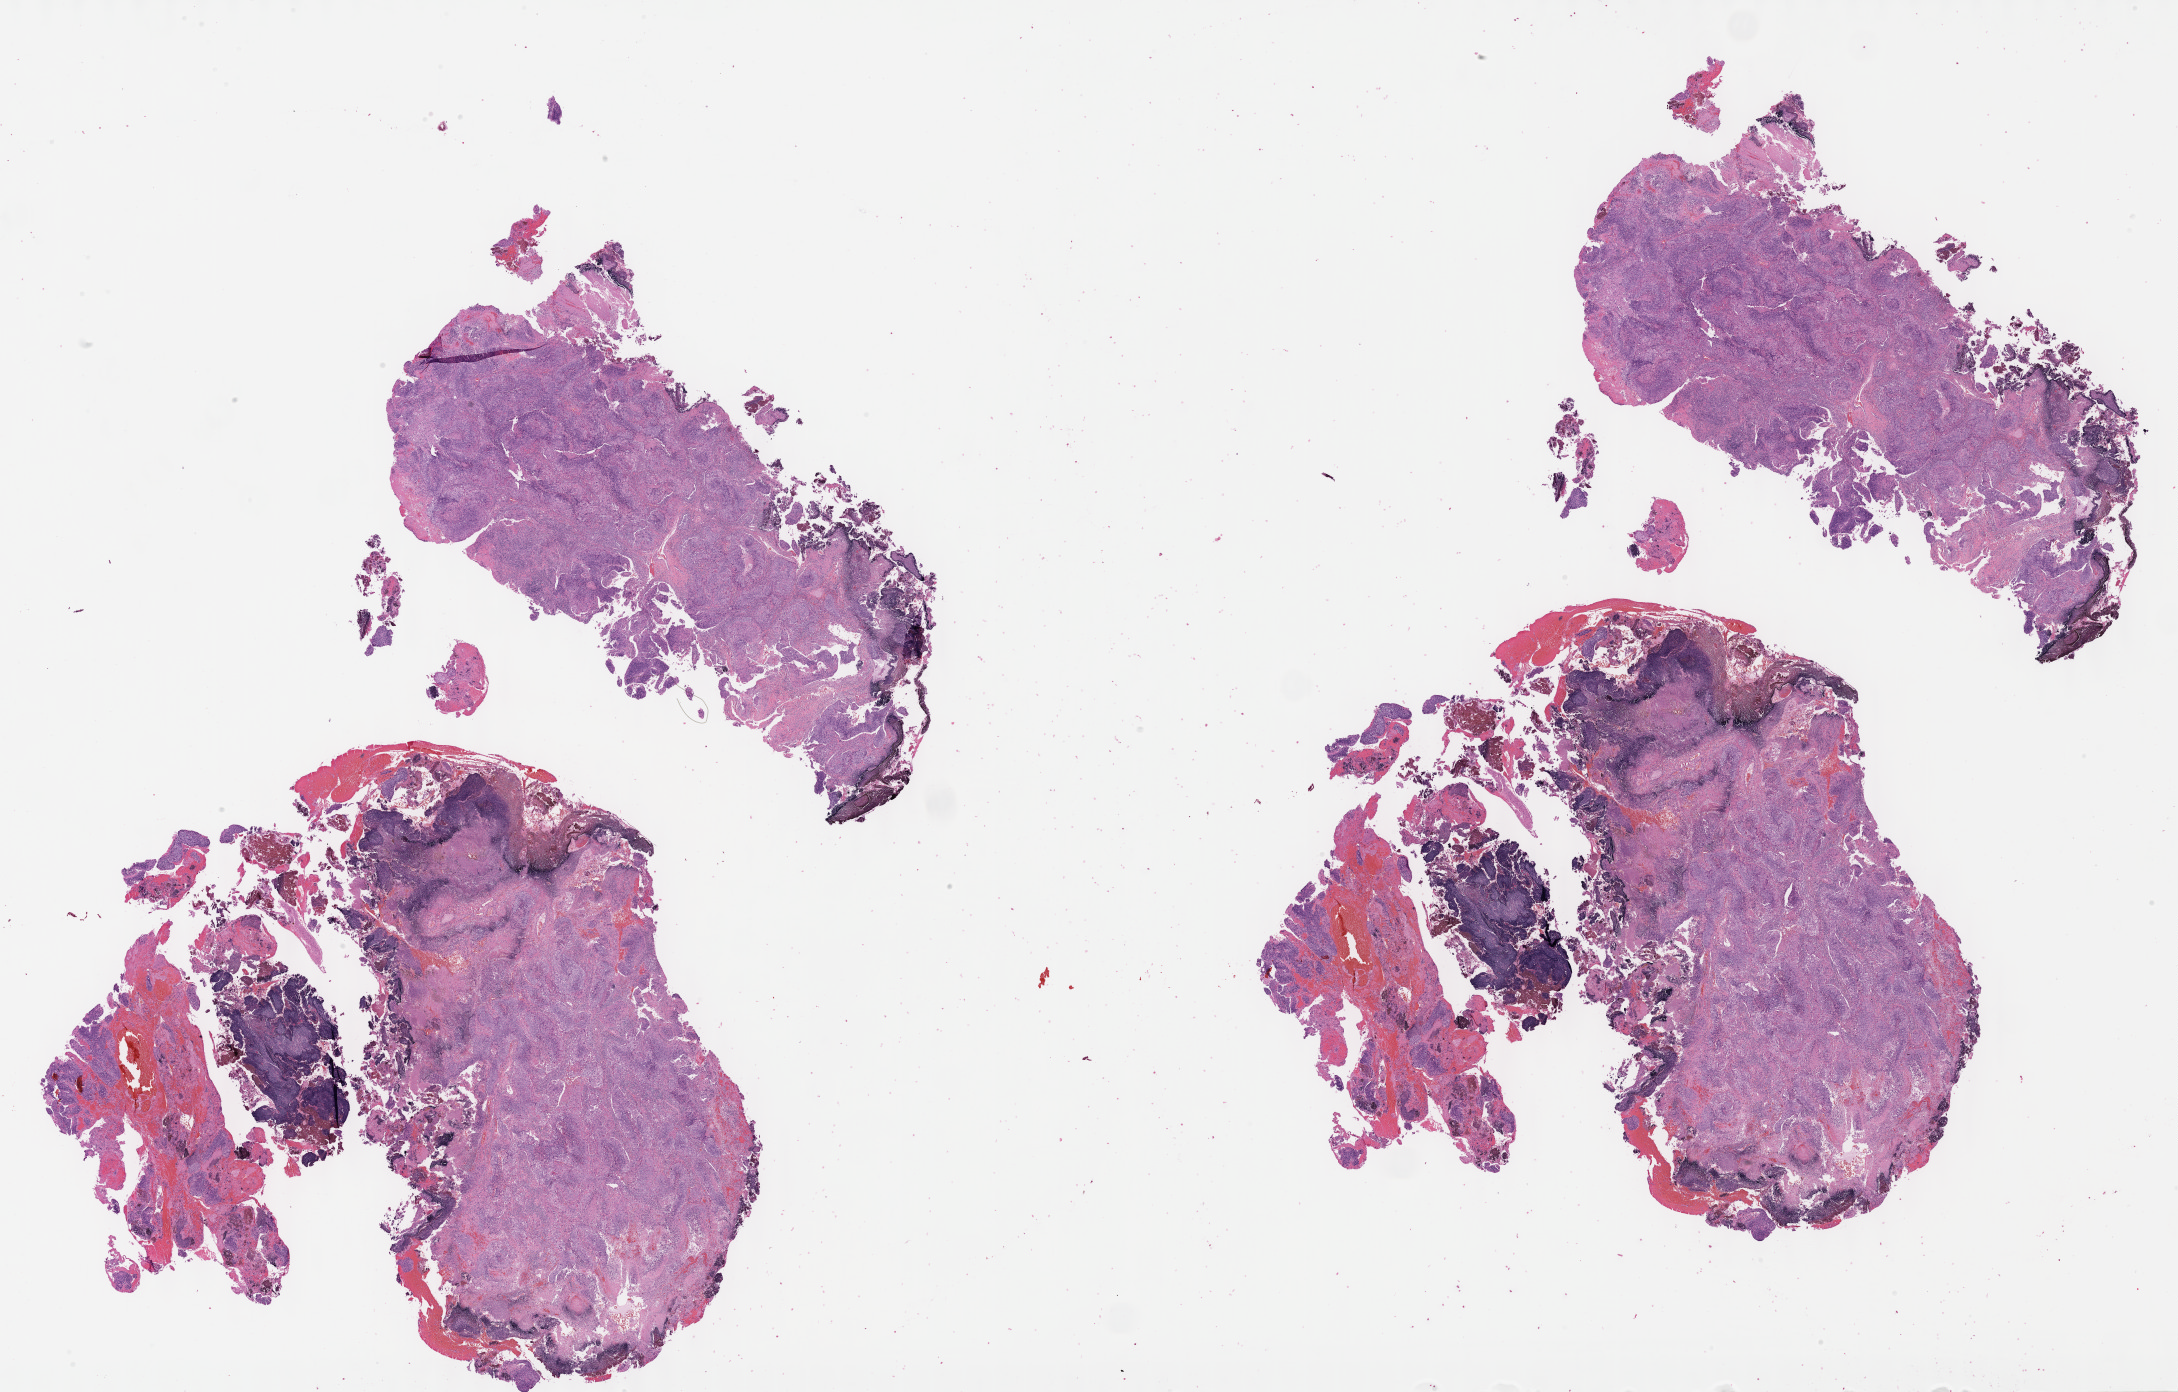
Digitized H&E-stained tissue section (whole slide) — shown as a low-resolution overview of the whole scanned area (about 35.2 x 22.5 mm, slide scanned at 40x). FFPE section. Primary tumour sample from the cervix. Patient: female, age at initial diagnosis 50 years. Histologic grade: G2 (moderately differentiated).
Pathologic diagnosis: Squamous cell carcinoma, NOS (cervix uteri). FIGO stage: IIIB.